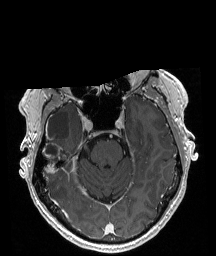
Brain MRI from a brain-tumour surgery series, one axial slice. Slice 134 of 208 in the series (ordered by position). T1-weighted post-contrast. 1 mm slice thickness. 216 × 256 image matrix, field of view 211 × 250 mm. From the clinical record (not read from this slice): histopathology: Astrocytoma; WHO grade: 4; IDH mutation: yes; tumour location: Right Temporal.
Structures marked on this image (manually delineated by an expert):
- tumour: box from (x=42, y=143) to (x=60, y=173) px